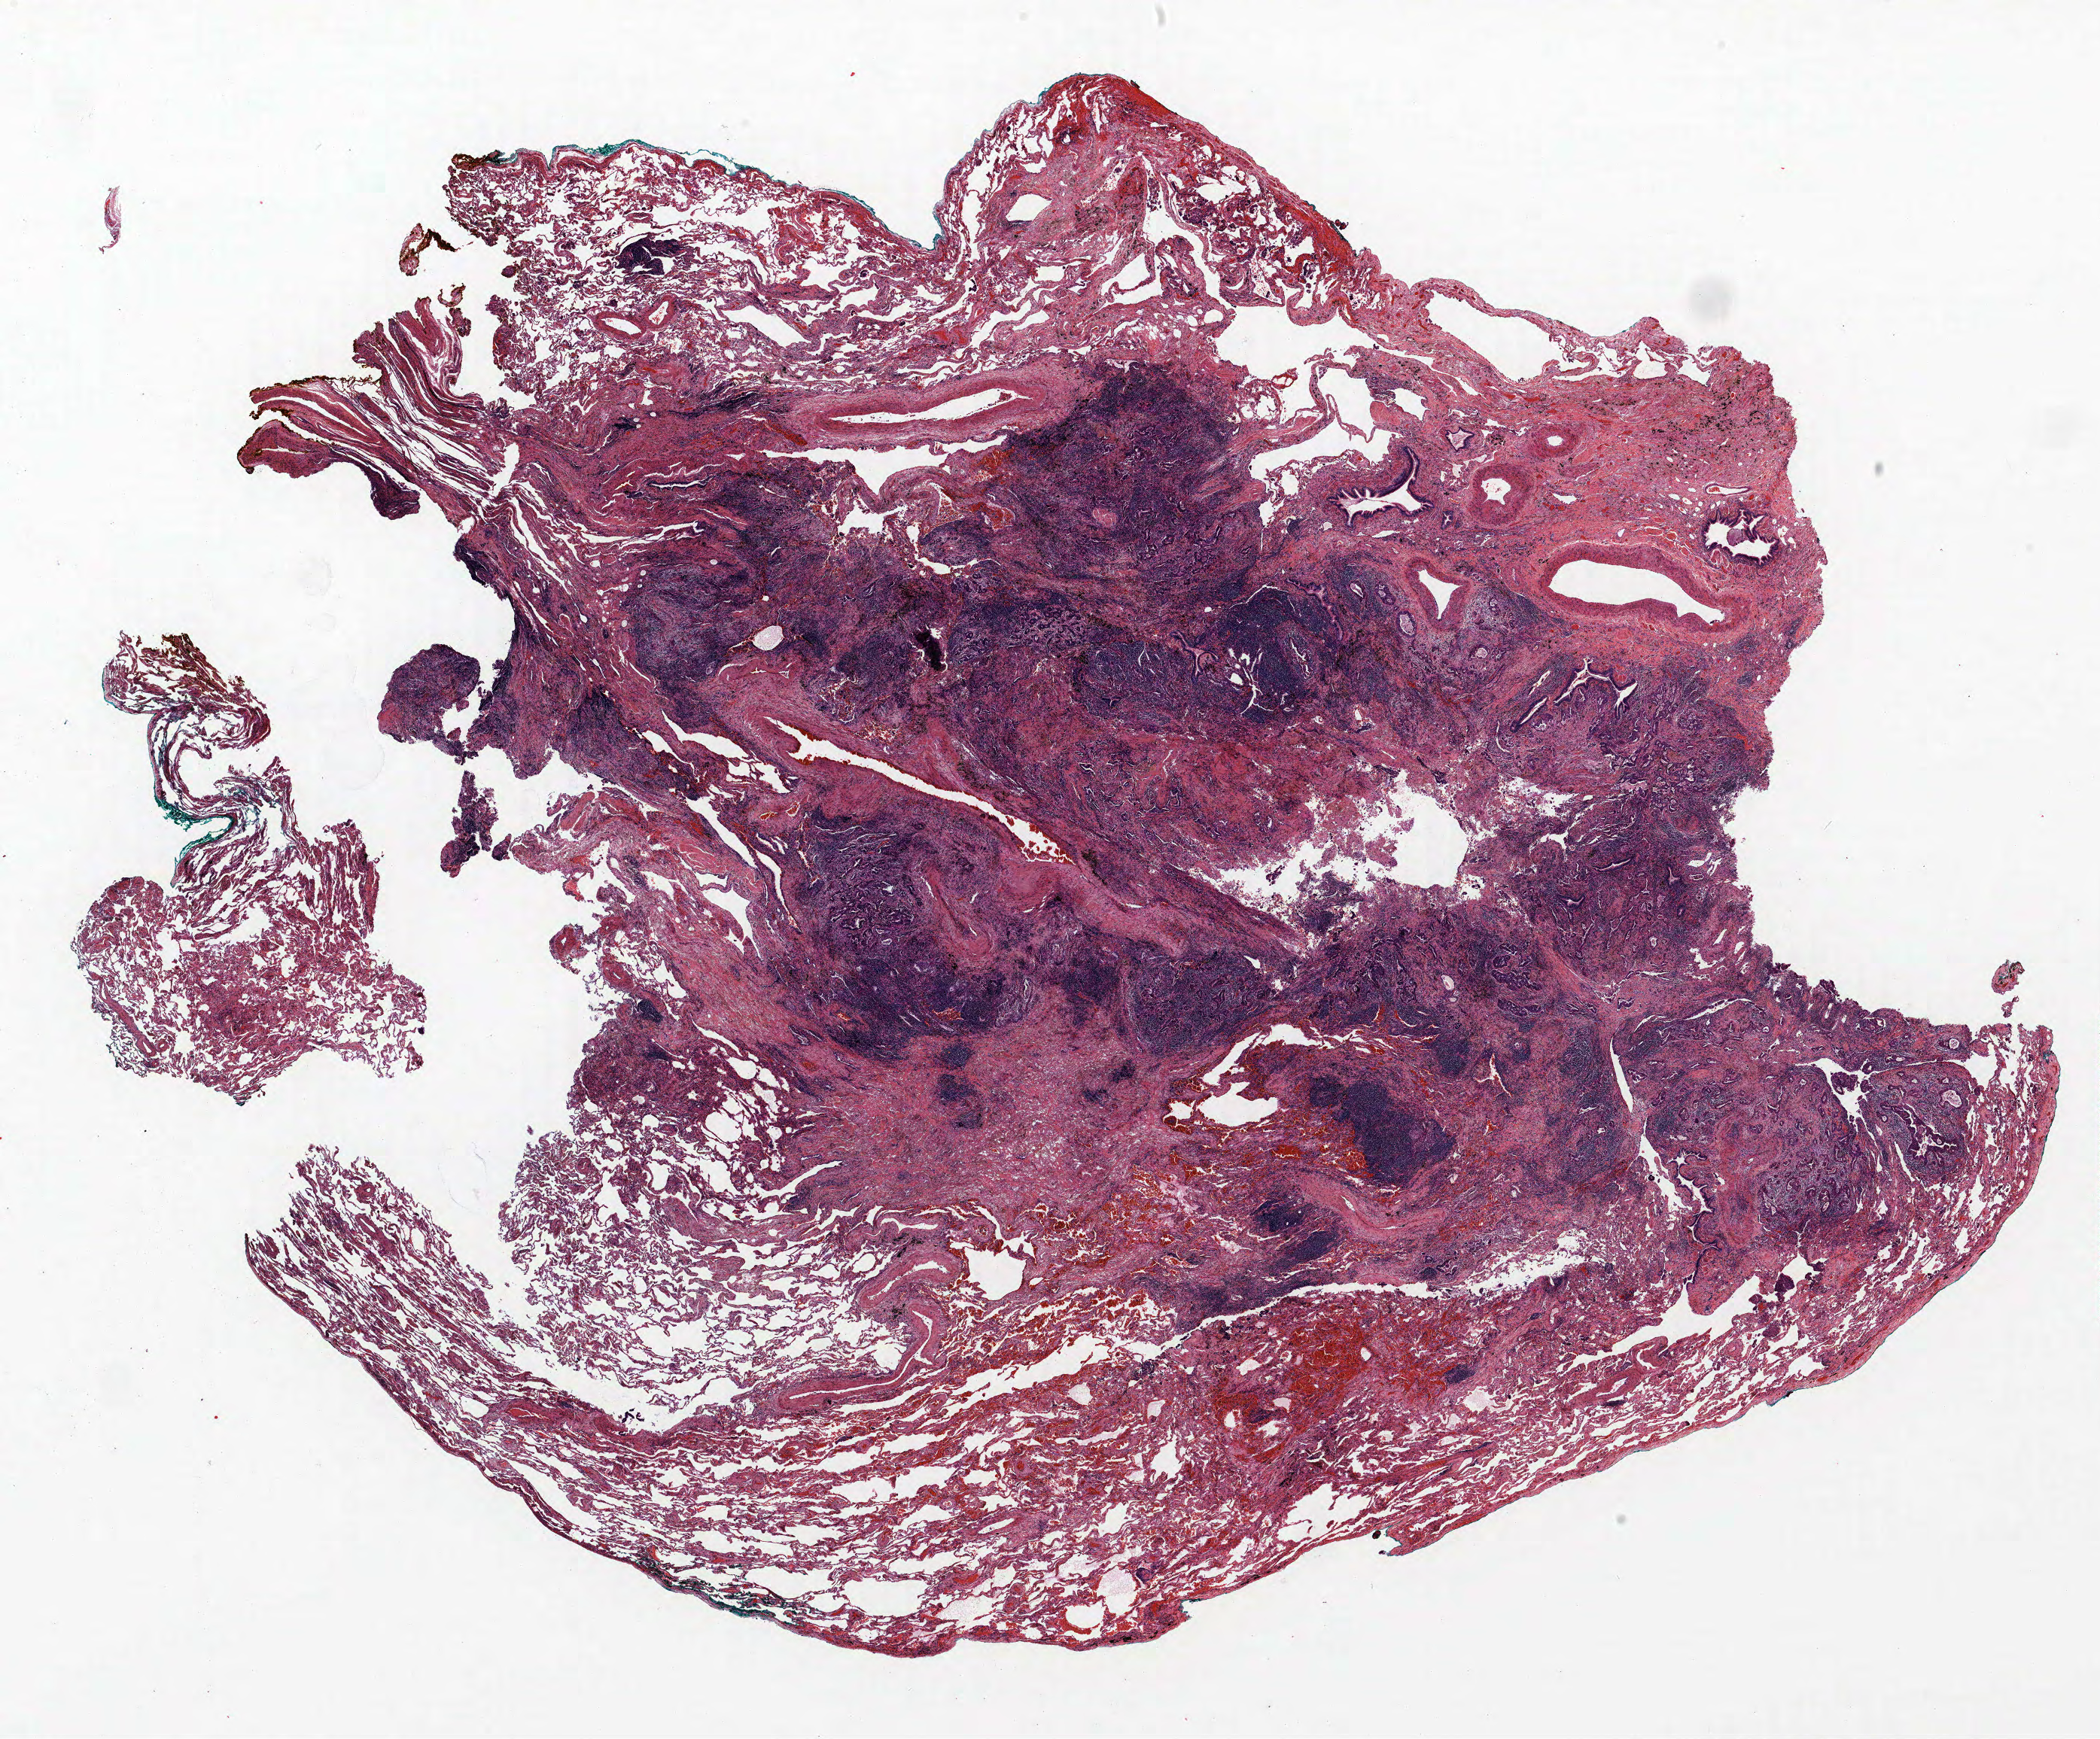
H&E whole-slide image, low-resolution overview of the scanned area, about 22.3 x 18.5 mm; FFPE section; lung tissue. Female, age 64 at enrolment. Former smoker at enrolment. Grade: moderately differentiated (G2).
- stage (AJCC 6th edition): IA
- primary tumour location (clinical record): left lower lobe
- participant's lung-cancer diagnosis: Adenocarcinoma, NOS
- tumour size (pathology): 17 mm